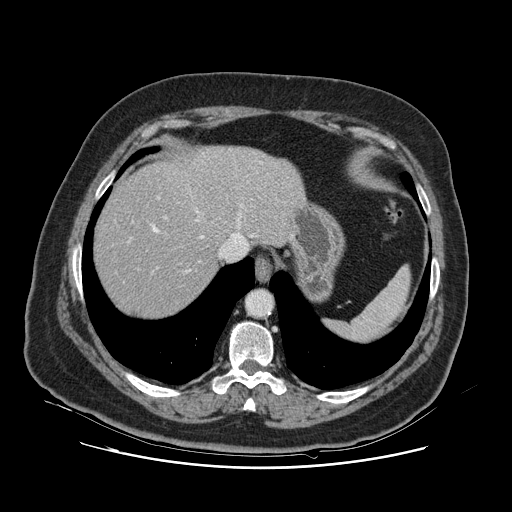
Contrast-enhanced abdominal CT, one axial slice. Position 101 of 132 along the scan axis. 120 kVp. Intravenous contrast given. Soft-tissue window (W 400 / L 40 HU). 512 × 512 image matrix. Female patient, age 73 years. From the clinical record (not read from this slice): diagnosis: colorectal cancer liver metastases, imaged before liver resection; multiple liver metastases: no; largest metastasis: 7 cm; disease in both lobes: no.
Structures marked on this image (manually delineated by an expert):
- hepatic veins: bounding box <129,209,240,272> (left, top, right, bottom; pixels)
- liver: <95,147,300,318>
- planned liver remnant (the part of the liver to remain after resection): <95,164,230,317>
- portal vein (with intrahepatic branches): <157,196,168,219>